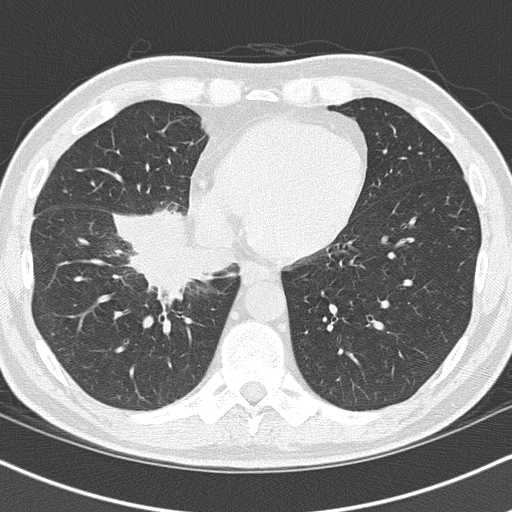
Low-dose screening chest CT, one axial slice; position 41 of 151 along the scan axis; lung window (W 1500 / L -600 HU); 2 mm slice thickness; 512 × 512 image matrix, field of view 320 × 320 mm.
Annotated regions visible in this slice (expert manual segmentation):
- lesion 1 (tumor, hilum of right lung): bounding box (x1, y1, x2, y2) in pixels: (124, 213, 193, 294)